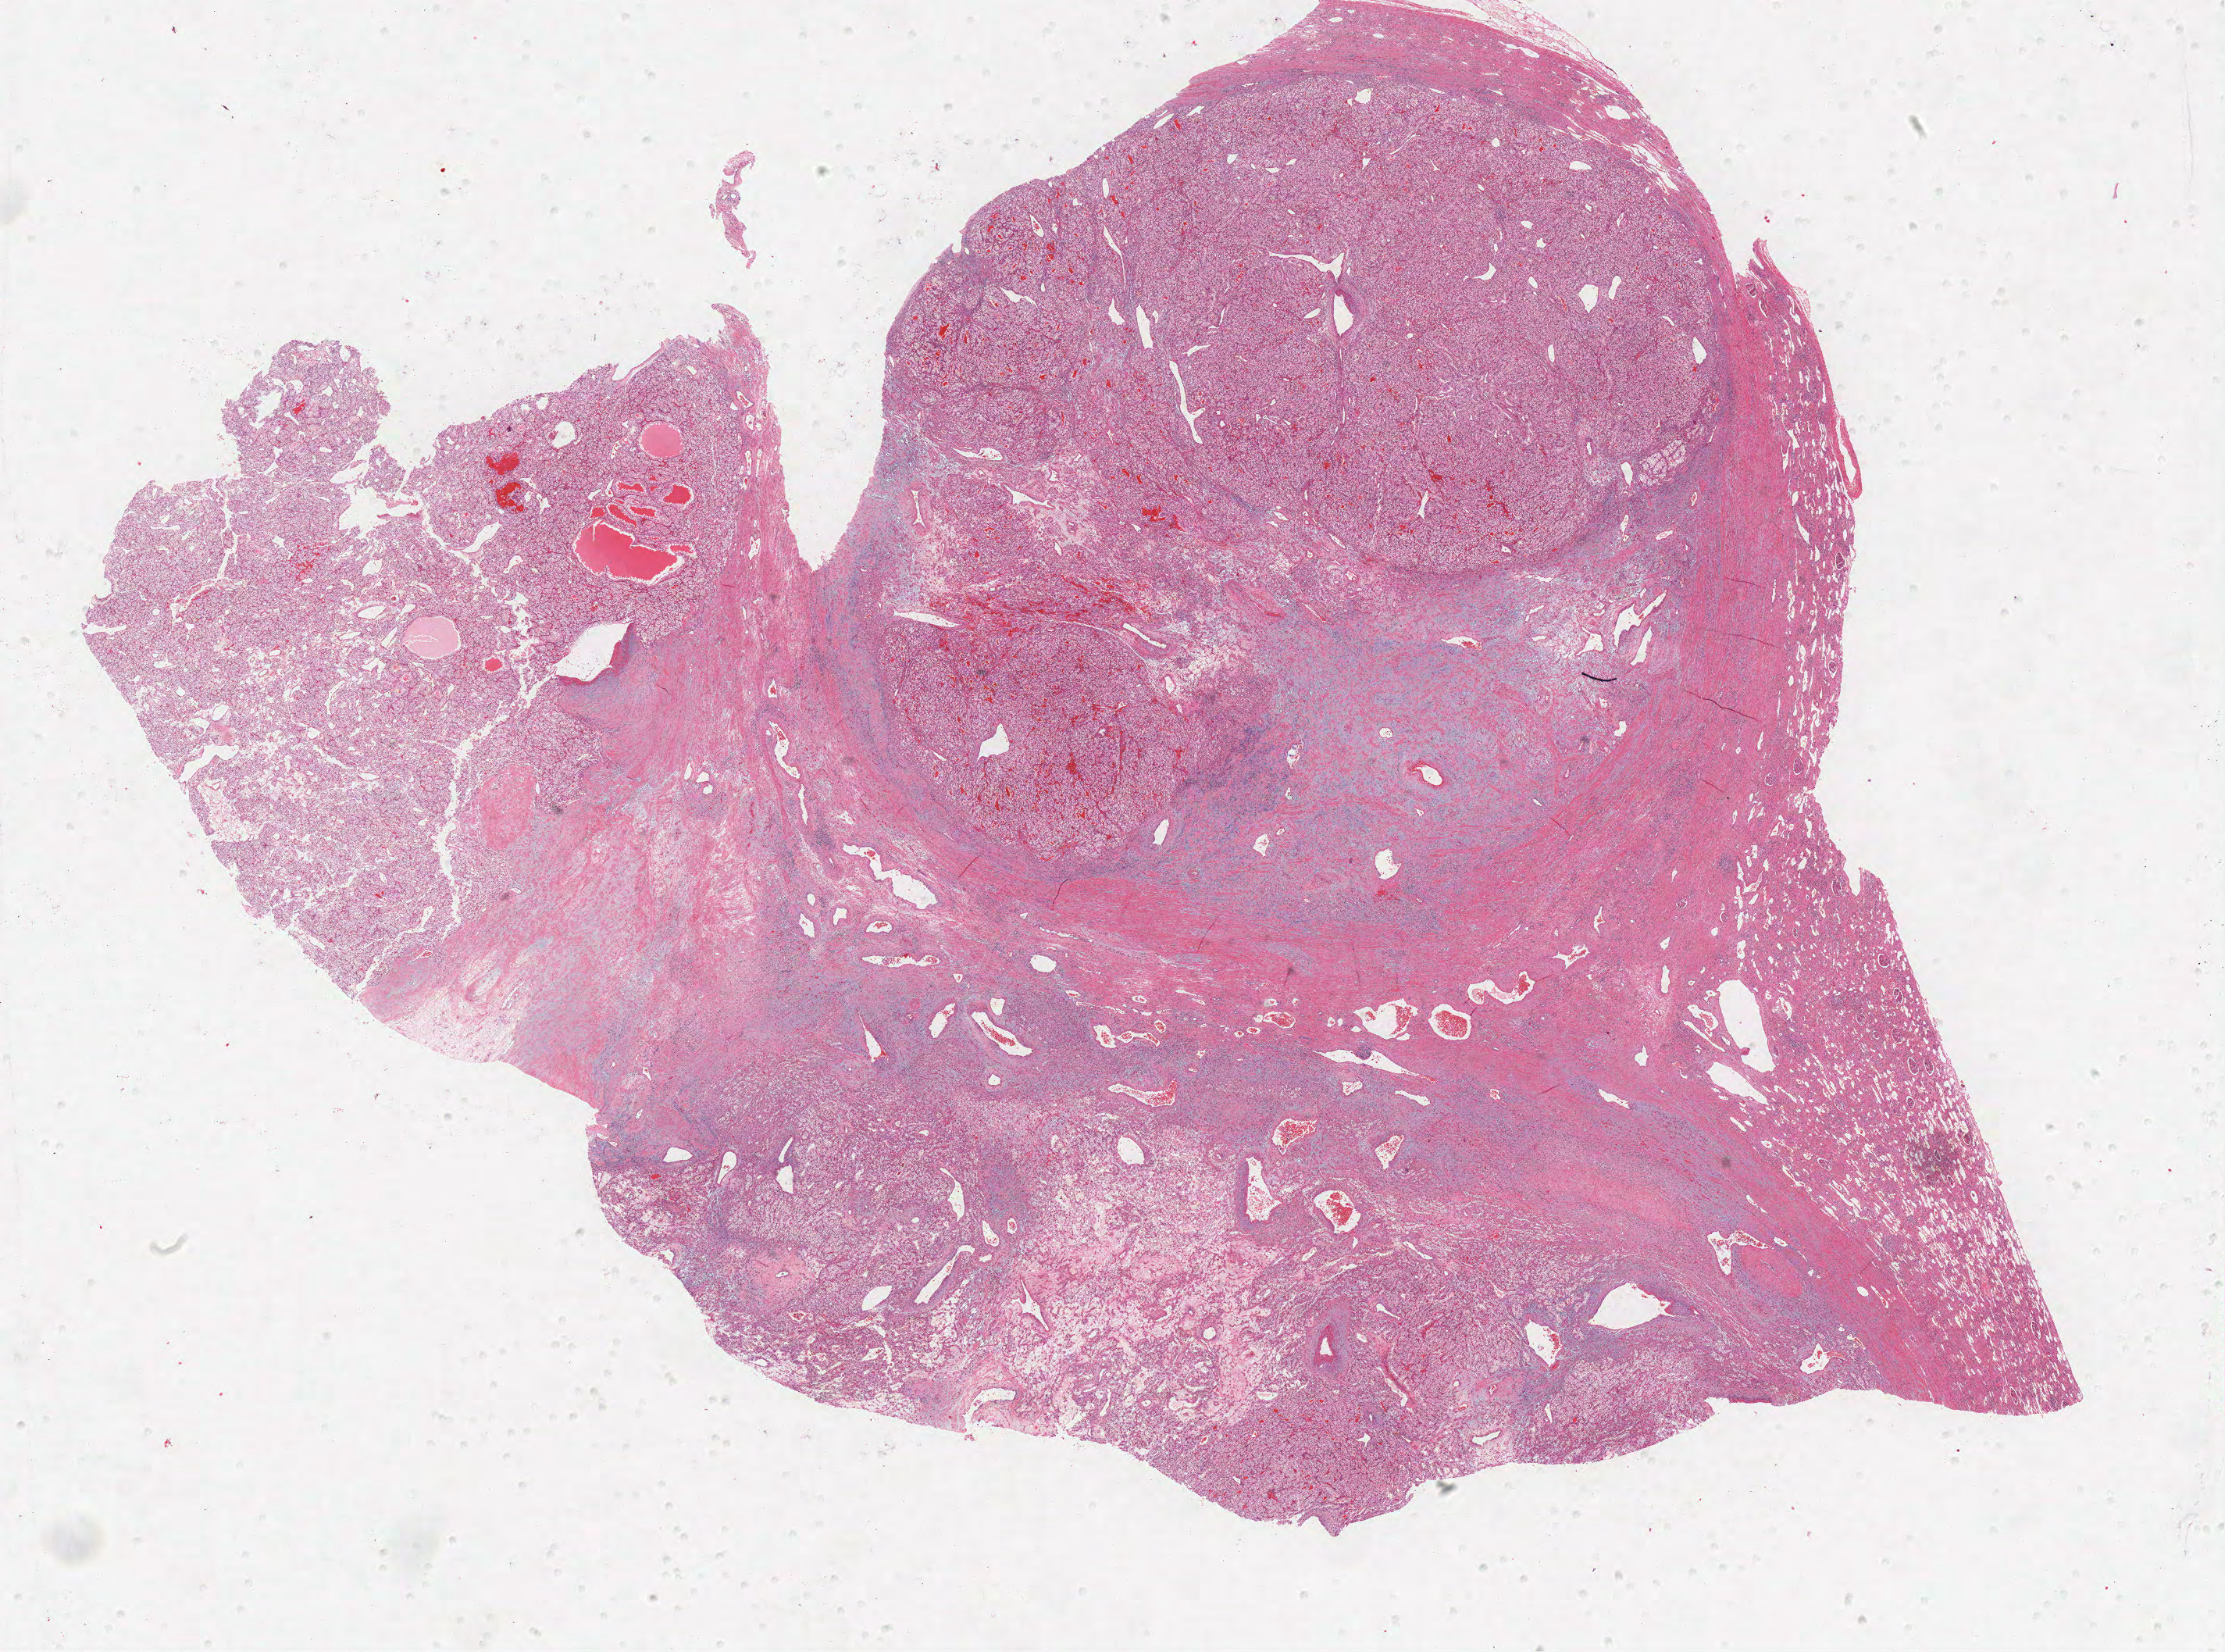
Hematoxylin and eosin (H&E) stained whole-slide image, shown as a low-resolution overview of the whole scanned area (about 22.8 x 16.9 mm, slide scanned at 40x), formalin-fixed paraffin-embedded (FFPE) diagnostic section, kidney, primary tumour sample. Male patient; age at initial diagnosis 40 years. Histologic grade: G3 (poorly differentiated).
Histologic diagnosis: Clear cell adenocarcinoma, NOS. AJCC pathologic stage: I.